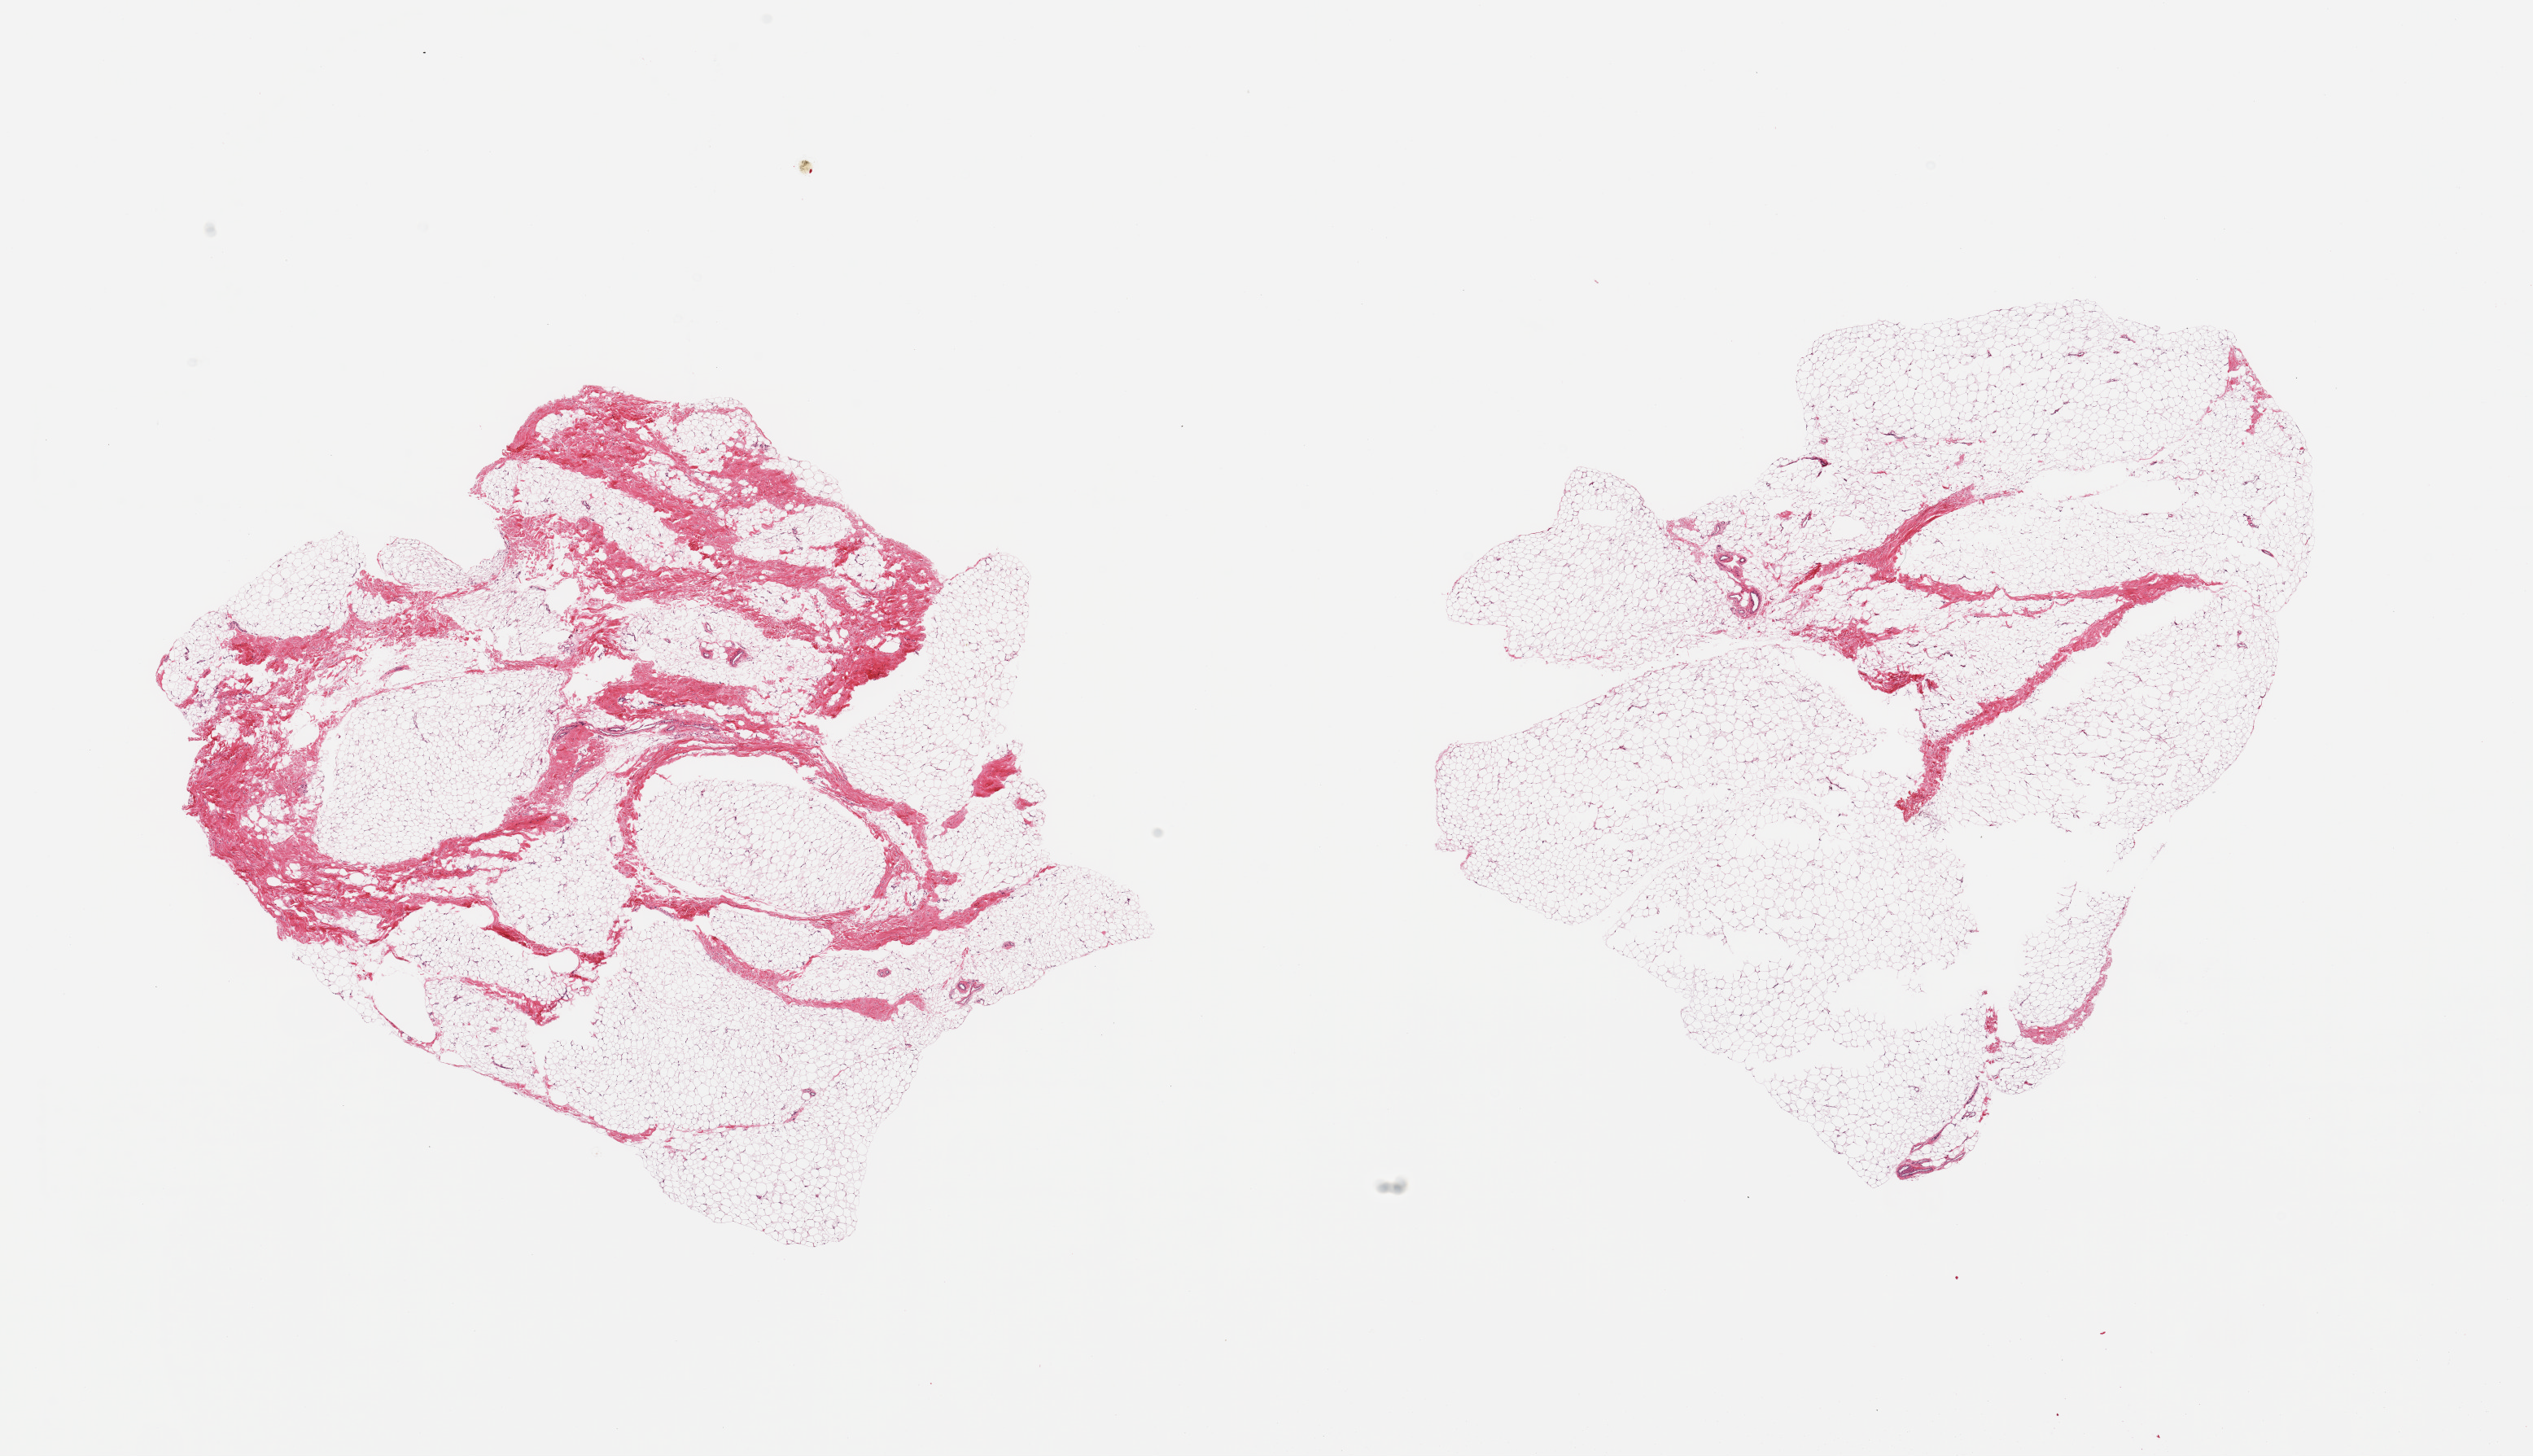
Digitized hematoxylin and eosin (H&E)-stained section — shown as a low-resolution overview of the whole scanned area (about 24.6 x 14.1 mm); PAXgene-fixed paraffin-embedded (PFPE) section; target tissue: breast; donor tissue sample.
- reviewer comment on this tissue sample: 2 pieces, ifibroadipose elements only